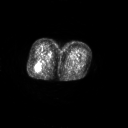
FDG PET of an extremity soft-tissue mass (from a PET/CT study), one axial slice. Position 26 of 267 along the scan axis. 128 × 128 image matrix. Patient: female, 70 years. Case-level facts recorded for this patient, not image findings: histological type: synovial sarcoma; grade: intermediate; site of the primary tumour: right buttock.
Outlined on this slice (expert contour drawn on MRI and transferred to this co-registered scan by the dataset authors):
- gross tumour volume including surrounding oedema: bounding box <35,61,40,71> (left, top, right, bottom; pixels)